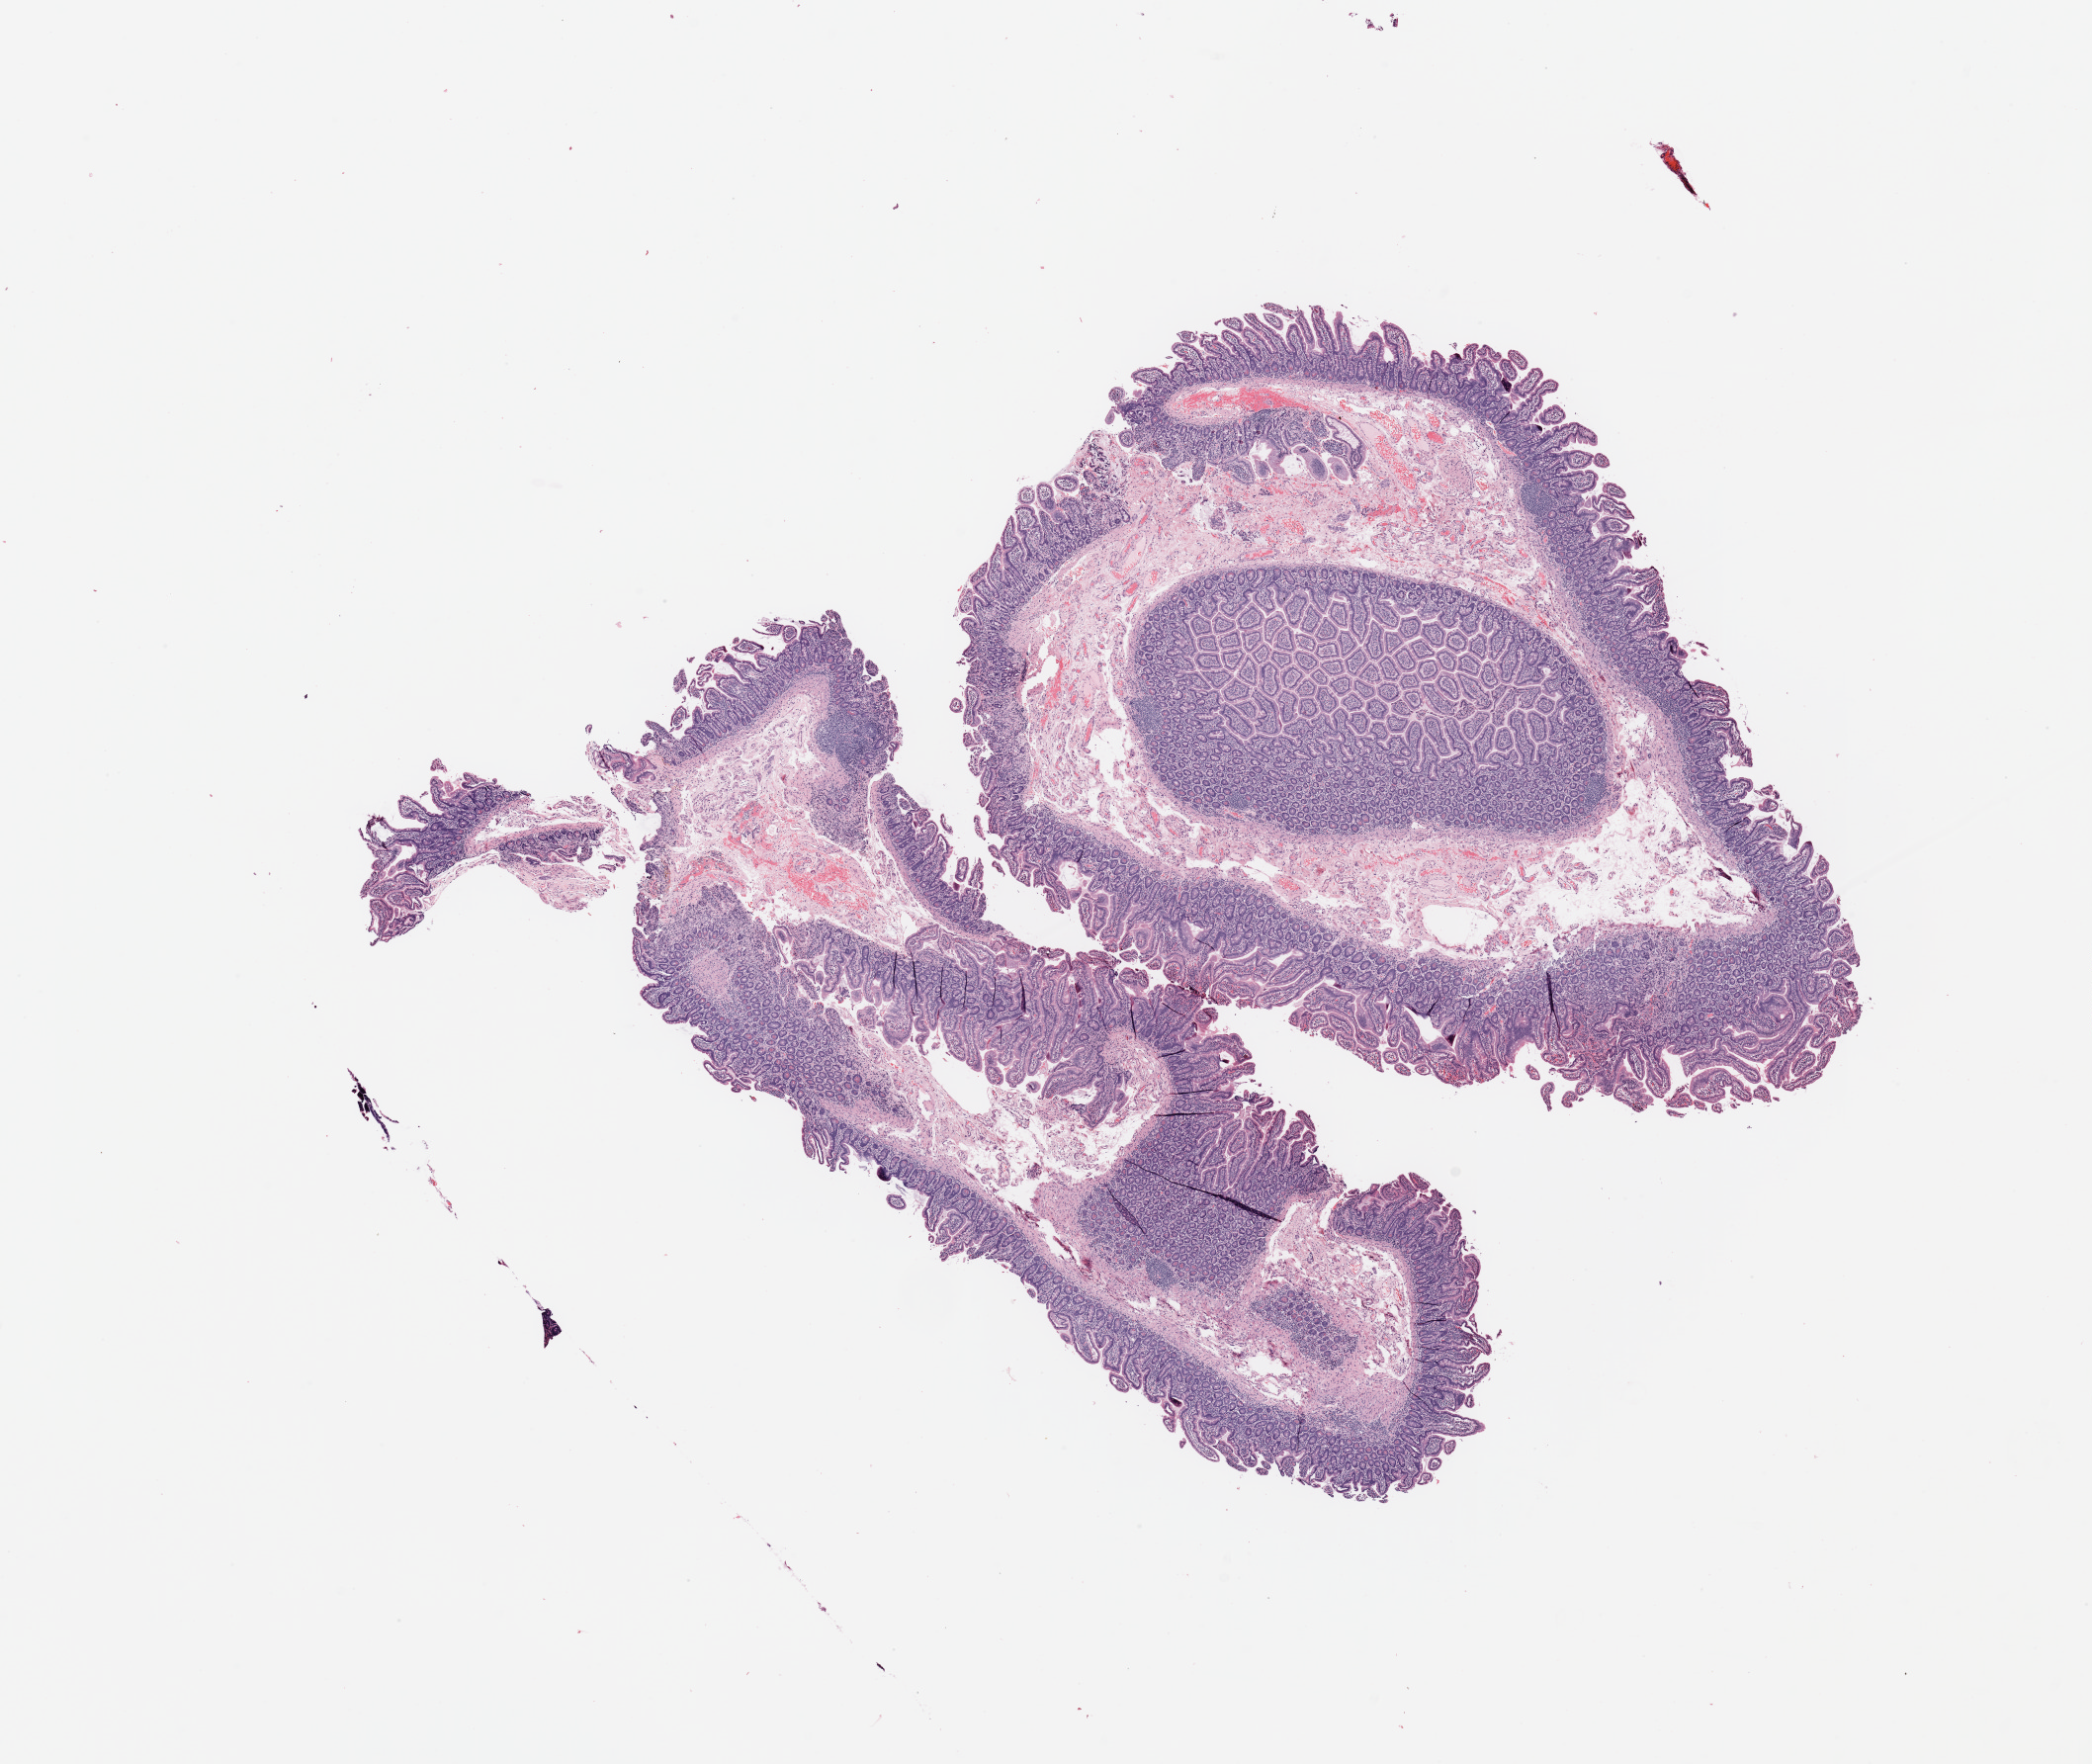
H&E-stained whole-slide image — a low-resolution overview of the entire scanned area, about 16.7 x 14.1 mm, normal (non-tumour) tissue sample, sampled site: pancreas. Female, 73 y/o.
This section: normal (non-tumour) tissue from the same patient. Patient diagnosis: Infiltrating duct carcinoma, NOS.